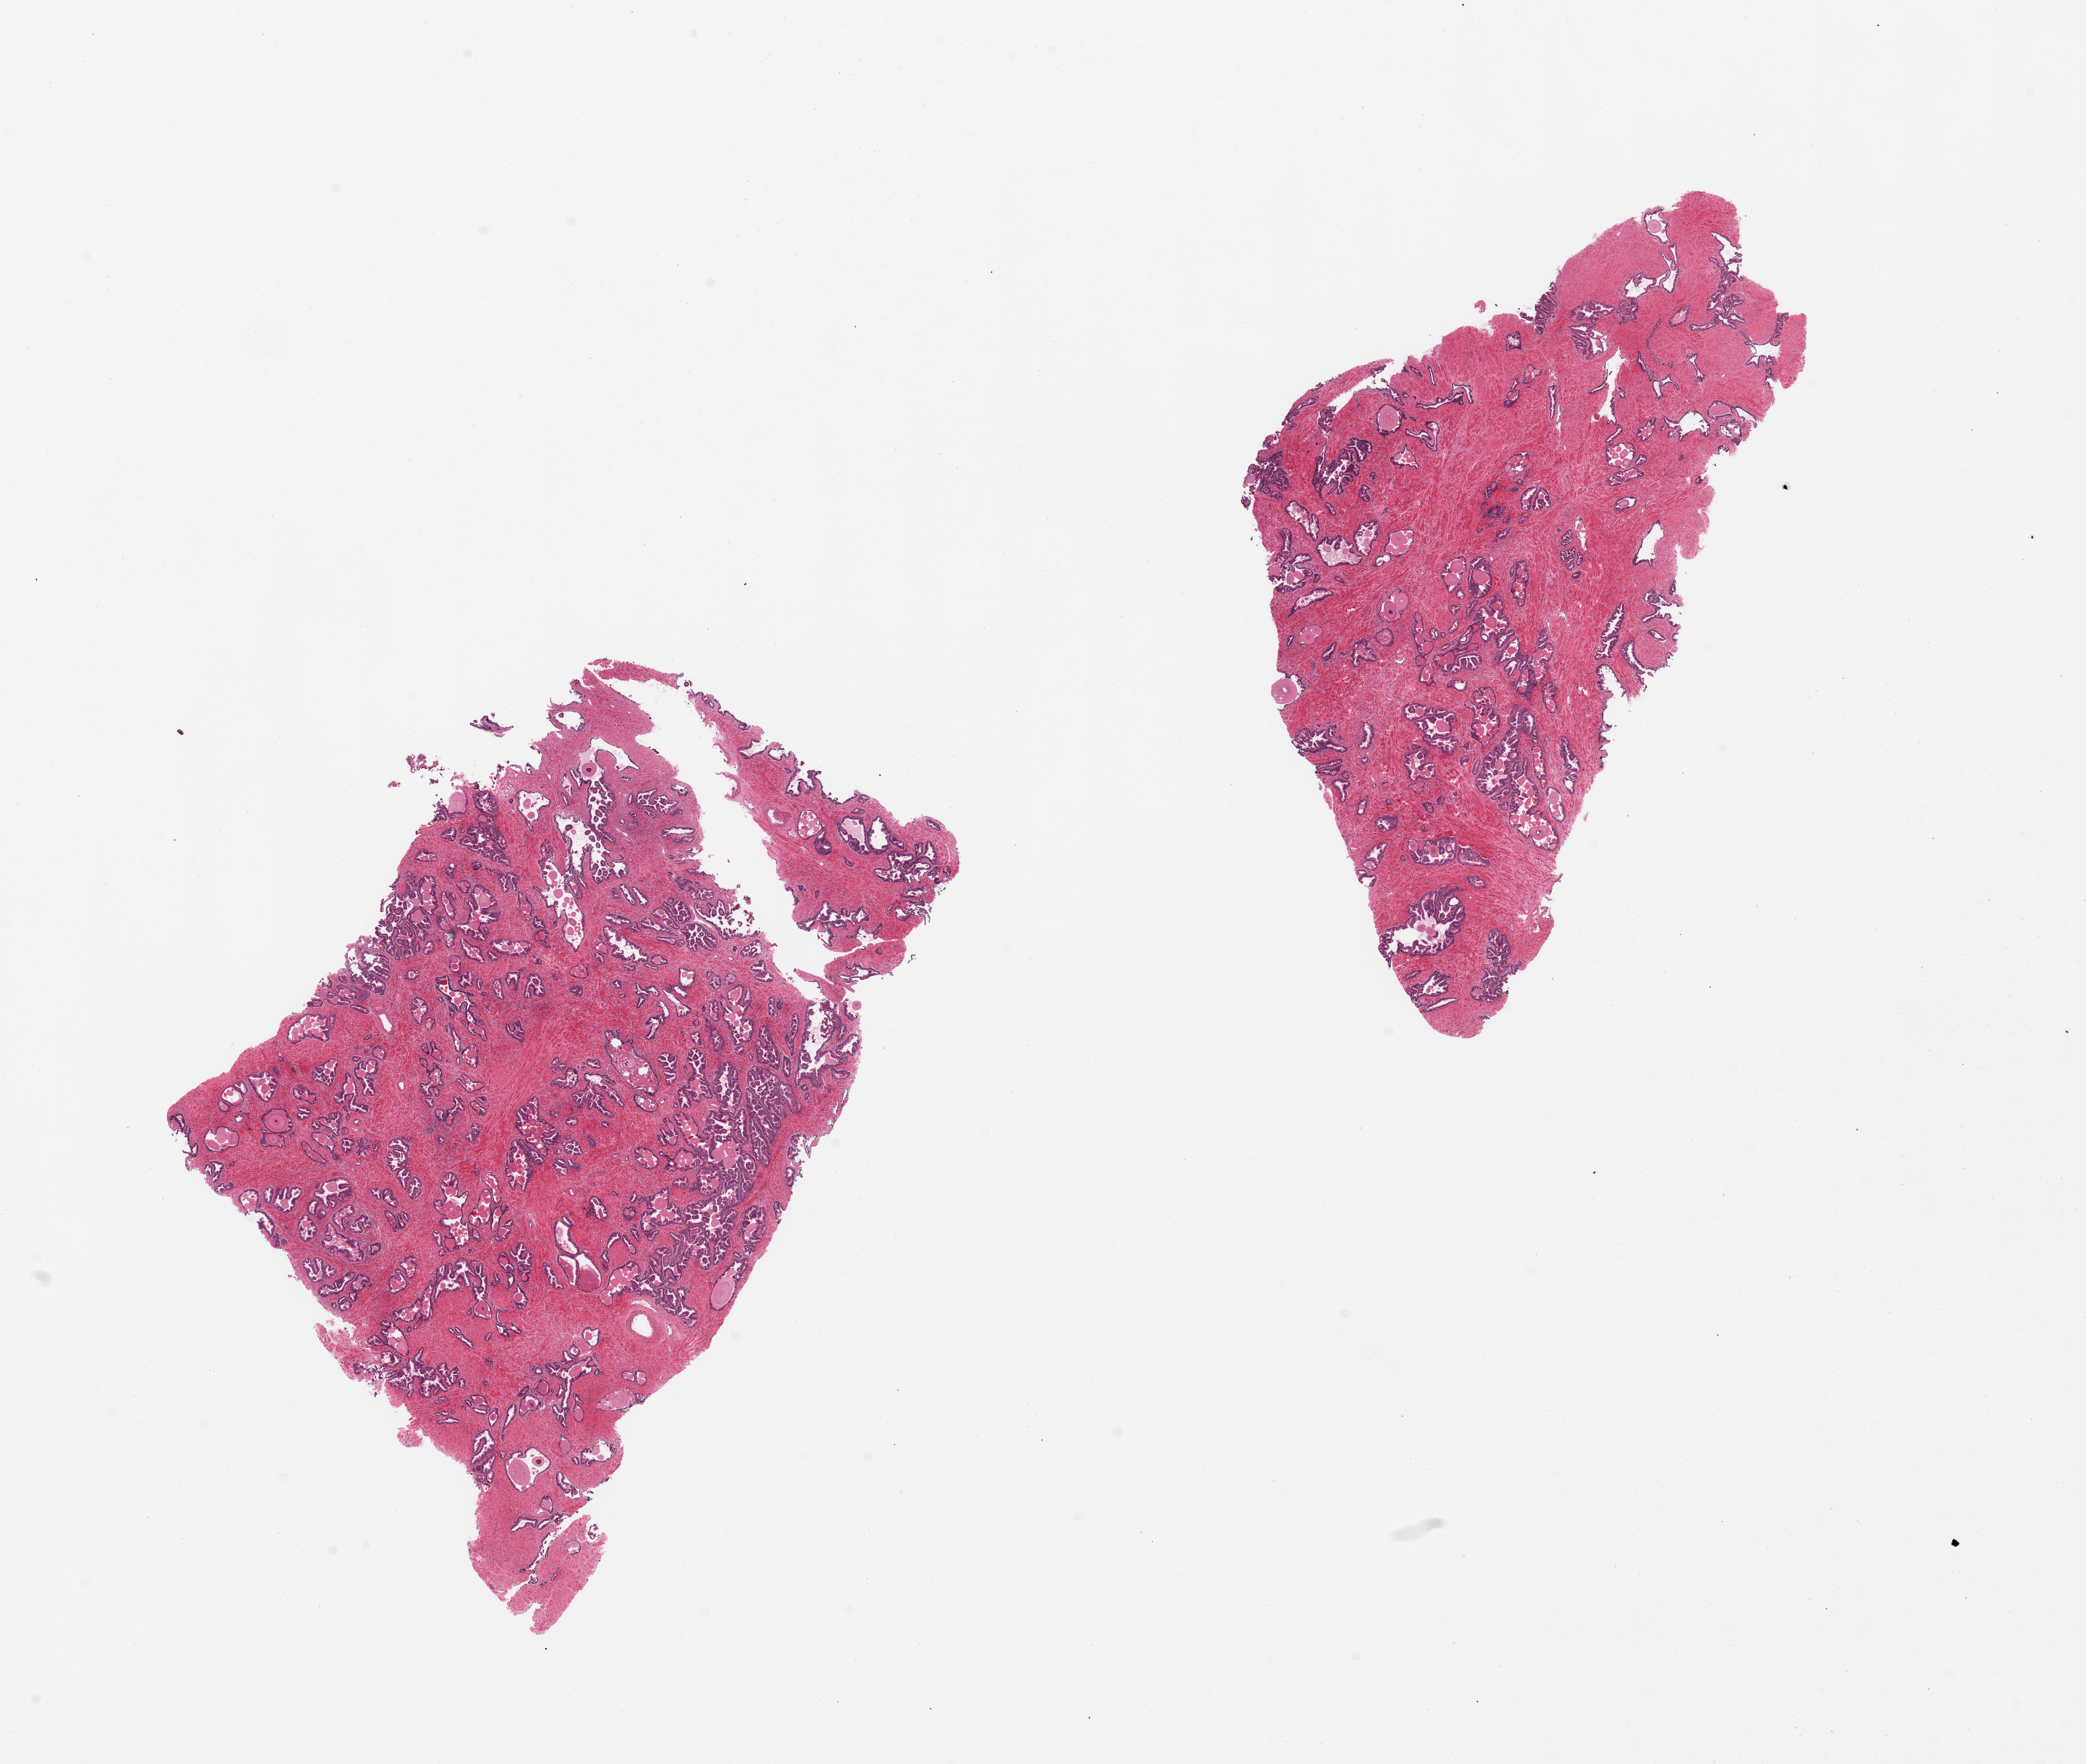
Whole-slide image, haematoxylin and eosin stain, brightfield — whole scanned area (about 22.6 x 19.1 mm, from a 20x scan) shown as a low-resolution overview. PAXgene-fixed paraffin-embedded (PFPE) section. Target tissue: prostate. Tissue donor sample. Donor sex: male.
• review note (as recorded): 2 pieces; glandular hyperplasia